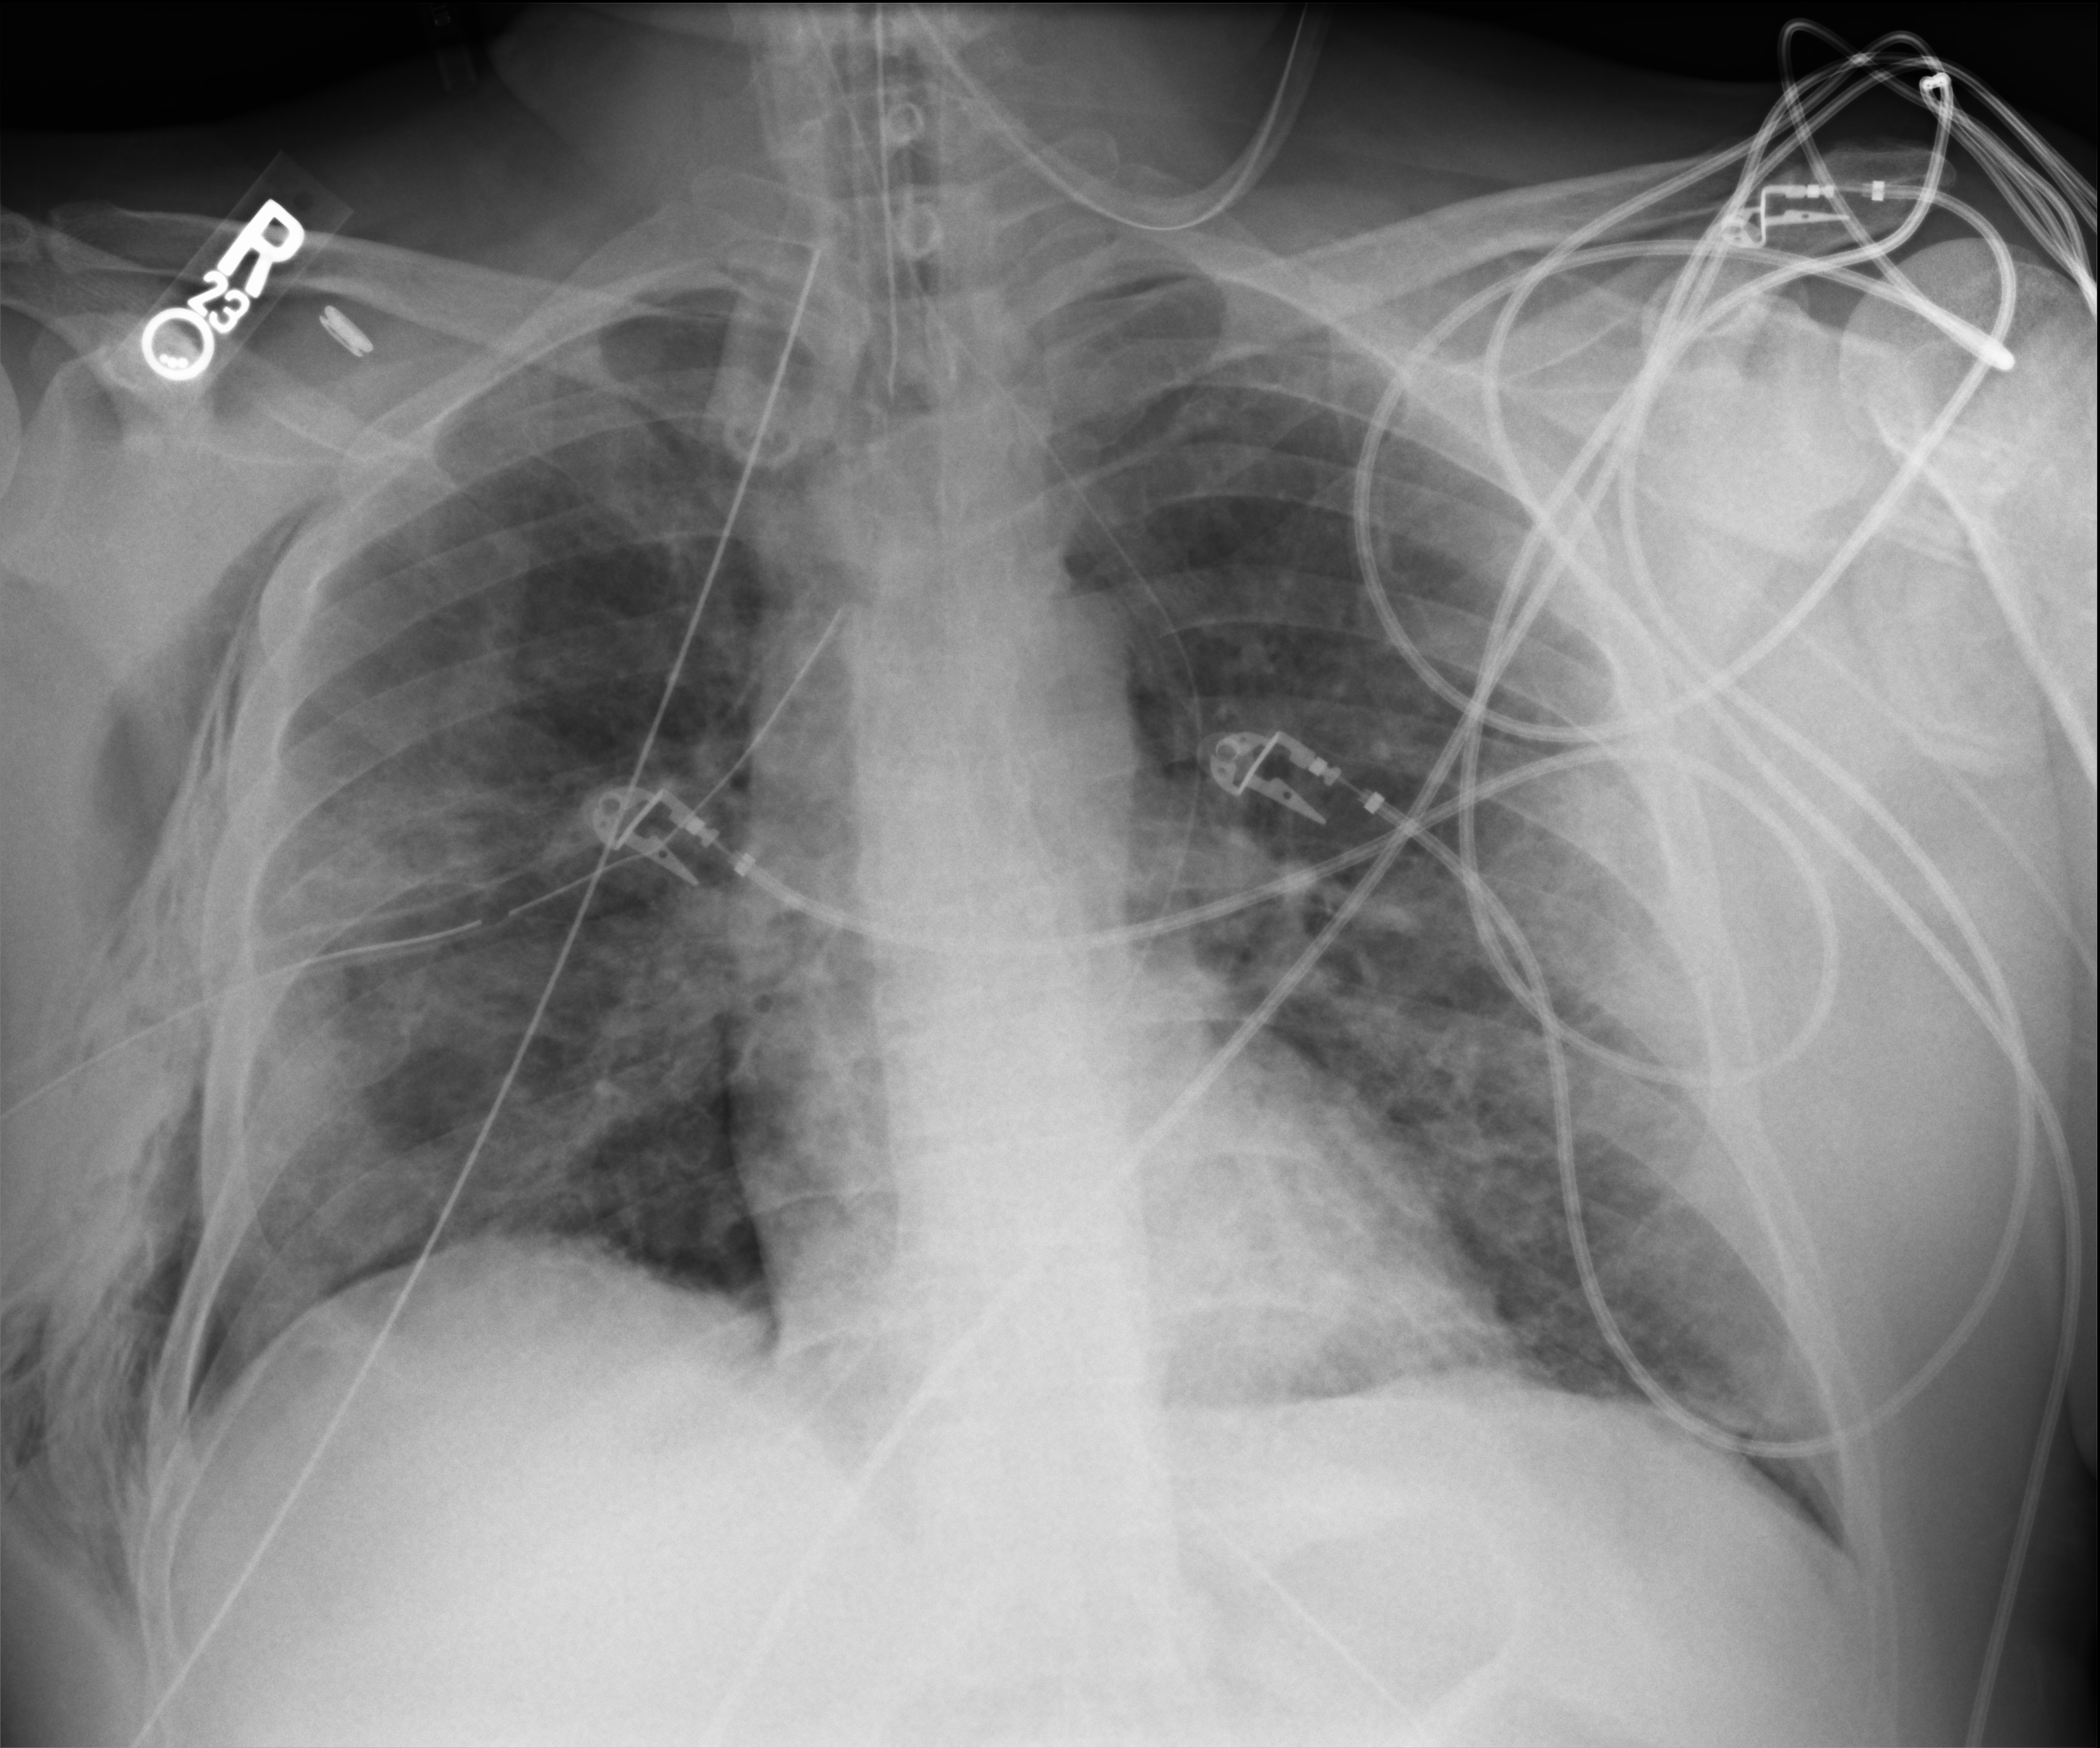
Chest X-ray (portable), anteroposterior (AP) projection. Patient hospitalised with COVID-19; male, aged 18–59 years.
Admission-level facts for this patient (not findings on this image; timing relative to this image not recorded):
- admitted to intensive care during this hospital stay: yes